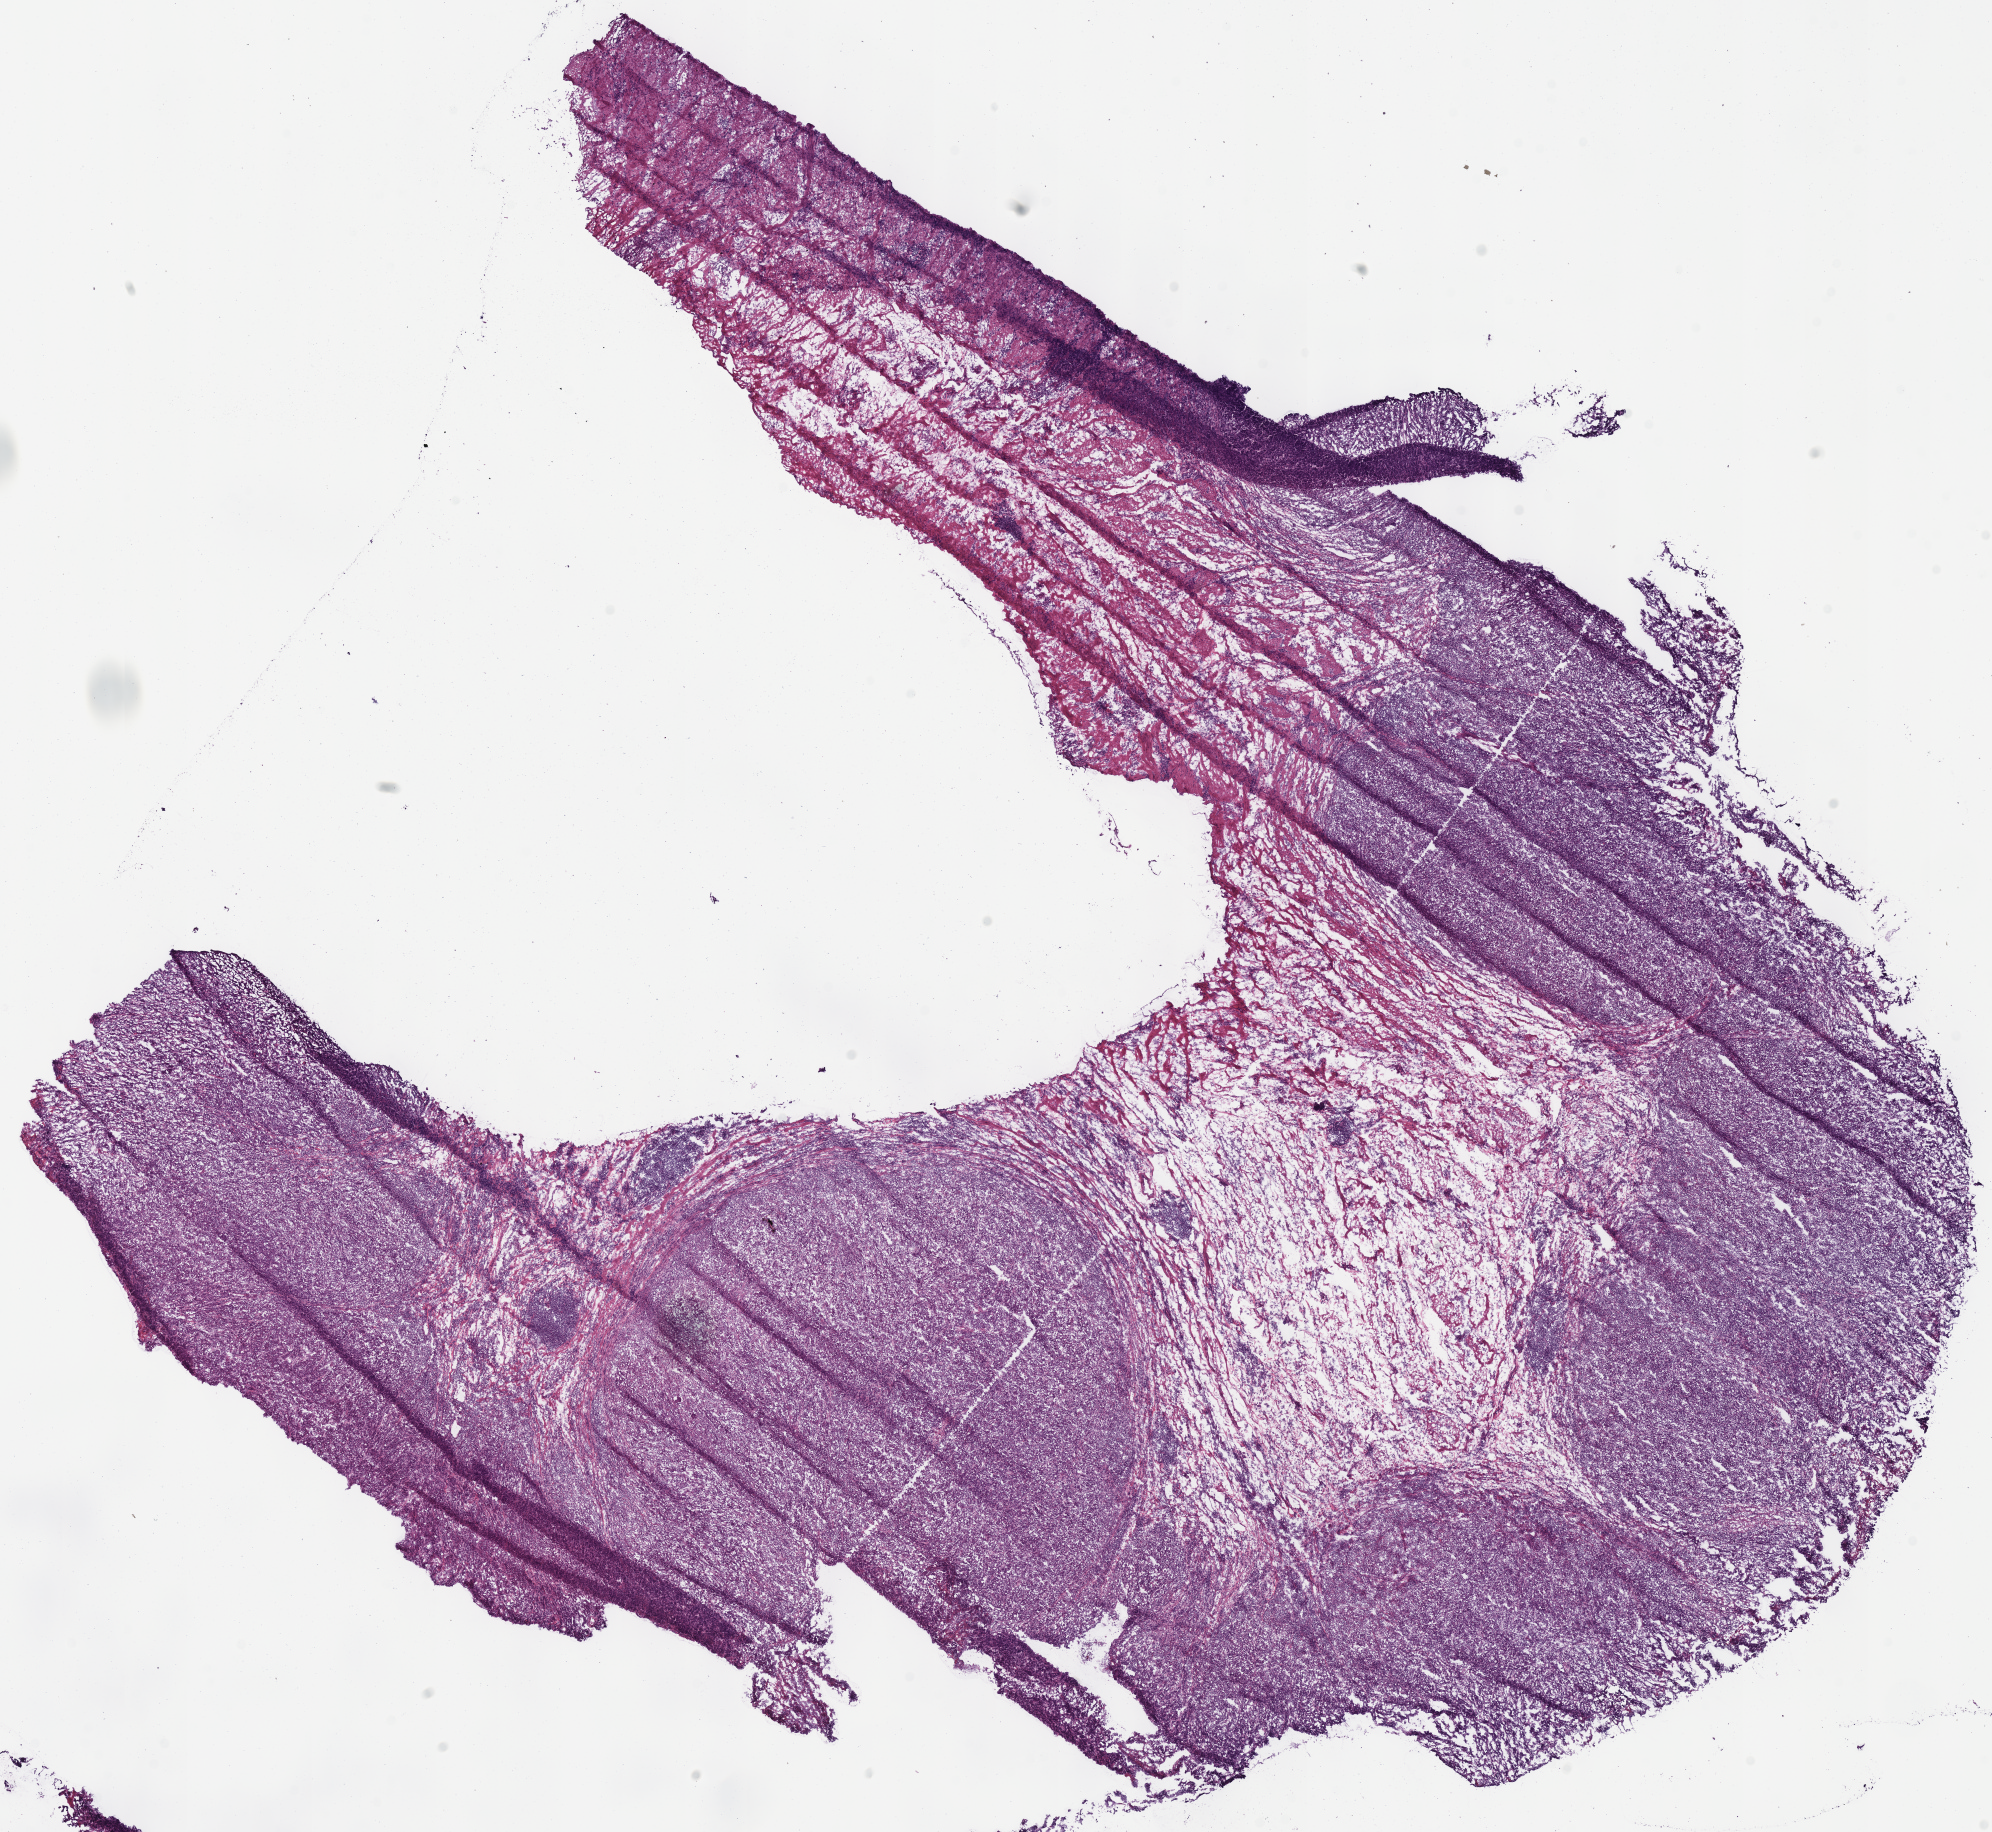
Whole-slide histology image, H&E — low-resolution overview of the scanned area, about 15.7 x 14.4 mm (slide scanned at 40x). Frozen section from the bottom of the tissue portion. Stomach, primary tumour sample. Female, age 73 years at initial diagnosis. Histologic grade: G3 (poorly differentiated). Pathologist review of this section (percent, as recorded): tumour cells 75%, tumour nuclei 55%, normal cells 0%, stromal cells 25%, necrosis 0%.
* diagnosis: Adenocarcinoma, NOS (fundus of stomach)
* AJCC pathologic stage: IB